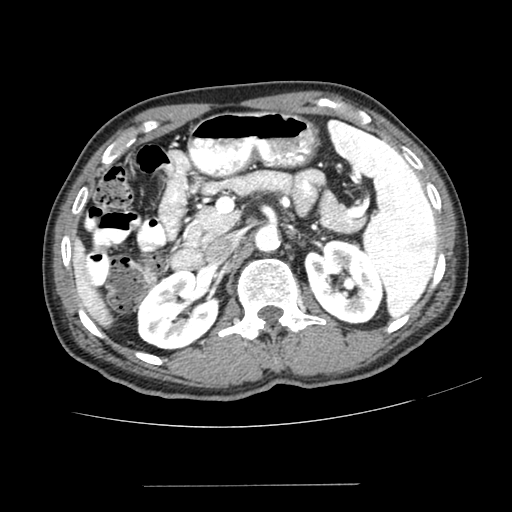
Contrast-enhanced abdominal CT (liver protocol), one axial slice. Slice 136 of 187 in the series (ordered by position). Reconstruction kernel SOFT. 100 kVp. One of 2 acquisitions stored at this slice position. Soft-tissue window (W 400 / L 40 HU). 2.5 mm slice thickness. 512 × 512 image matrix, field of view 360 × 360 mm. From the clinical record (not read from this slice): diagnosis: hepatocellular carcinoma (patient treated with transarterial chemoembolisation; whether this scan precedes or follows treatment is not stated here); TNM stage (as recorded): Stage-I; Child-Pugh class: A; tumour differentiation: poorly differentiated; tumour size: 1.6 cm.
Structures marked on this image (semi-automatic segmentation, software-assisted and operator-edited):
- liver parenchyma outside the tumour (the mass and vessels are separate outlines, so this box may not span the whole liver): box from (x=72, y=239) to (x=112, y=326) px
- liver vessels: (x=78, y=248)–(x=91, y=305)